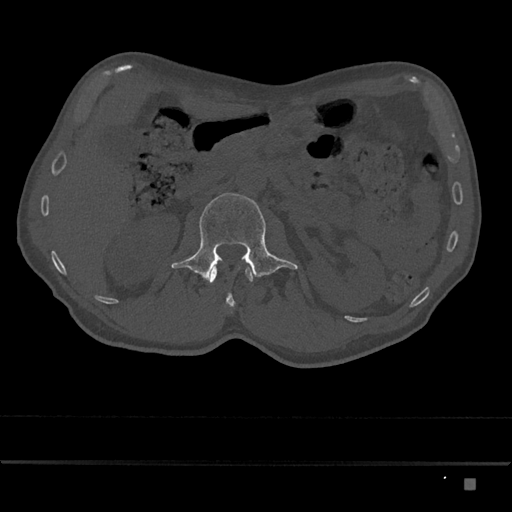
CT including the spine, one axial slice. Slice 494 of 797 in the series (ordered by position). Reconstruction kernel Br40s/3. Bone window (W 1800 / L 400 HU). 512 × 512 image matrix. Male patient, age 72 years. Case-level facts recorded for this patient, not image findings: primary cancer: prostate.
Annotated regions visible in this slice (semi-automatically segmented with operator editing):
- L1 vertebra: bounding box [x1, y1, x2, y2] px = [210, 266, 253, 307]
- L2 vertebra: [171, 193, 298, 282]